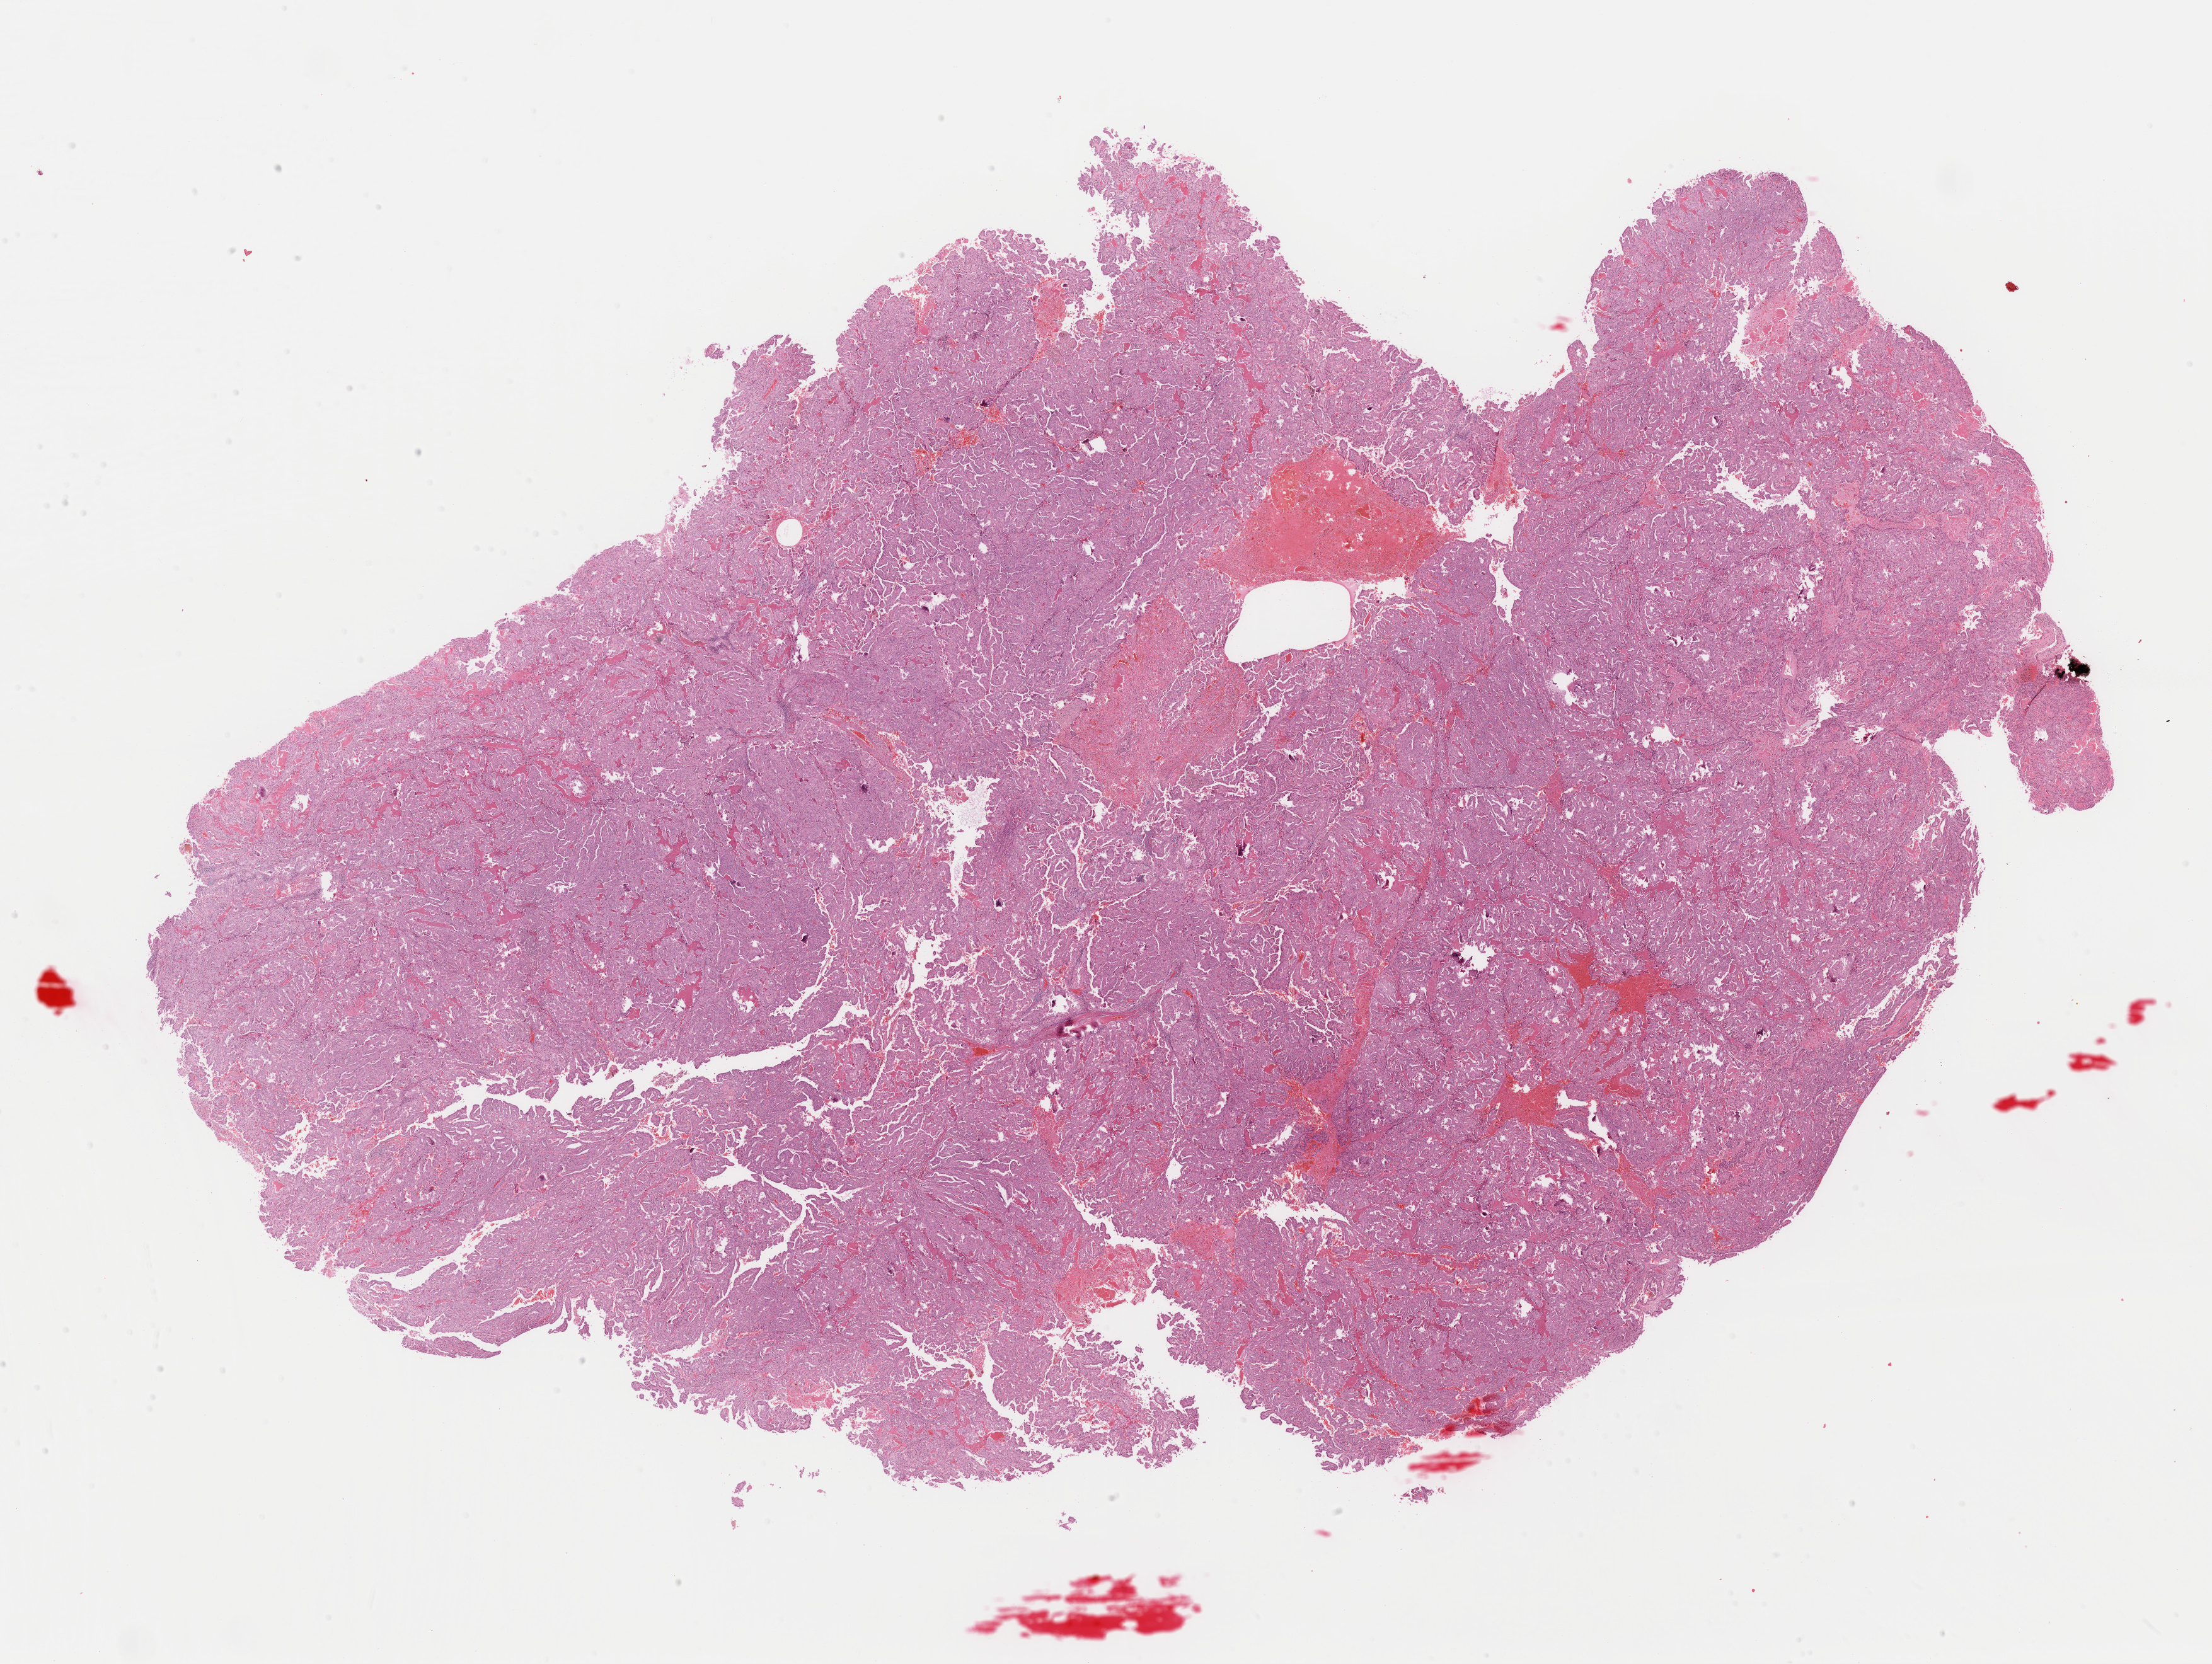
Digitized H&E-stained tissue section (whole slide) — low-resolution overview of the scanned area, about 27.7 x 20.9 mm, formalin-fixed paraffin-embedded (FFPE) diagnostic section, sample: primary tumour, thyroid. Female patient; age at initial diagnosis 75 years.
AJCC pathologic stage: IVA (7th edition). Pathologic diagnosis: Papillary adenocarcinoma, NOS (thyroid gland).